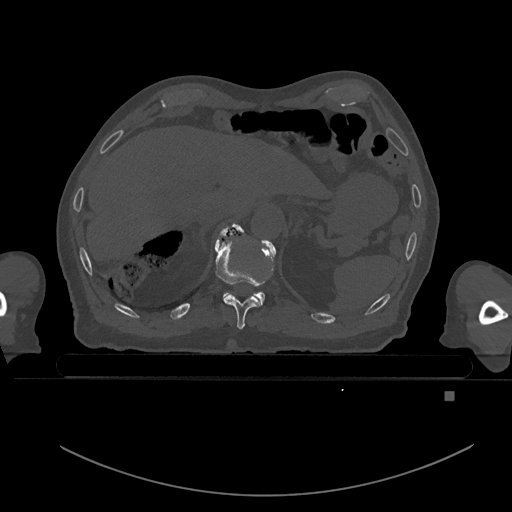
CT including the spine, one axial slice. Slice 68 of 969 in the series (ordered by position). Bone window (W 1800 / L 400 HU). 512 × 512 image matrix, field of view 456 × 456 mm. Male patient, age 82 years. From the clinical record (not read from this slice): primary cancer: prostate.
Outlined on this slice (semi-automatic segmentation, software-assisted and operator-edited):
- T10 vertebra: box from (x=215, y=224) to (x=266, y=330) px
- T11 vertebra: (x=219, y=223)–(x=273, y=305)